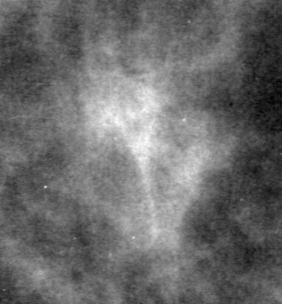
Cropped region of a digitized screen-film mammogram centred on a radiologist-marked abnormality; left breast; CC view.
Mass, shape irregular, margins ill defined; BI-RADS assessment category 4; subtlety rating 4 on a 1 (subtle) to 5 (obvious) scale; pathology (as recorded): malignant.